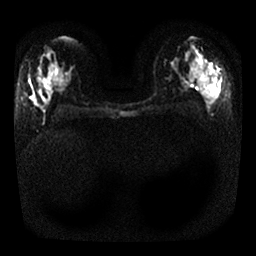
Breast MRI, one axial slice; slice 17 of 25 in the series (ordered by position); diffusion-weighted series; image 2 of 4 stored at this slice position (different b-values; order by instance number); 1.5 T; 4 mm slice thickness; 256 × 256 image matrix, field of view 320 × 320 mm. Female patient.
Structures marked on this image (expert manual segmentation):
- tumour on diffusion-weighted imaging: bounding box <203,61,210,70> (left, top, right, bottom; pixels)